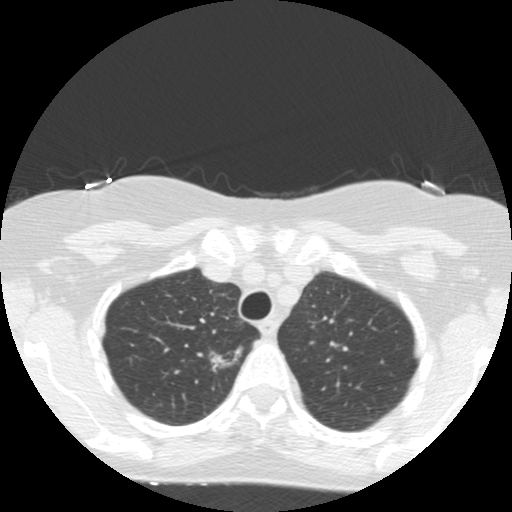
Low-dose screening chest CT, axial slice; baseline screening round; lung window (W 1500 / L -600 HU); 2.5 mm slice thickness; standard (soft-tissue) reconstruction kernel (STANDARD); slice 33 of 155 in the series. Female participant, aged 67 years at enrolment. Former smoker at enrolment.
- Lesion marked by an expert reader, bounding box <195,339,254,386> (left, top, right, bottom; pixels).
- The exam's reader record, not a measurement of the box and not confirmed to be the same lesion: non-calcified nodule or mass ≥4 mm, right upper lobe, 16 × 7 mm, poorly defined margins, mixed attenuation.
- Official screen result: positive, change unspecified: nodule(s) >= 4 mm or enlarging nodule(s), mass(es), or other non-specific abnormalities suspicious for lung cancer.
- Participant outcome: lung cancer diagnosed 132 days after this screen — adenocarcinoma, NOS, right upper lobe, moderately differentiated (G2), stage IA (AJCC 6th edition), 13 mm at pathology.